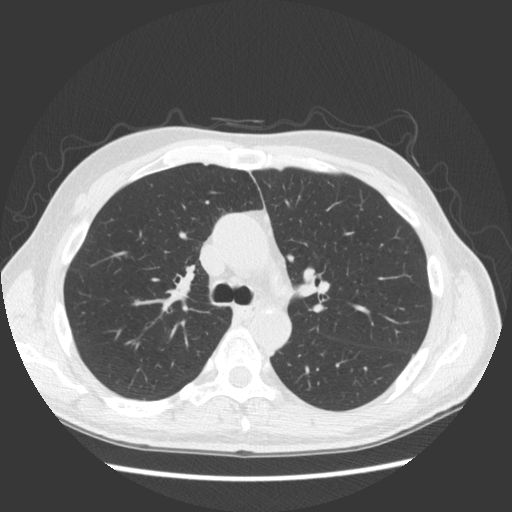
Chest CT (low-dose screening protocol), one axial image, second screening round (one year after baseline), lung window (W 1500 / L -600 HU), 2.5 mm slice thickness, slice 60 of 163 in the series. Male participant, aged 57 years at enrolment. Former smoker at enrolment.
Lesion marked by an expert reader, bounding box (x1, y1, x2, y2) in pixels: (154, 255, 204, 299). The screening reader recorded 3 non-calcified nodules or masses ≥4 mm on this exam; which of them this box marks is not recorded. Participant outcome: lung cancer diagnosed 264 days after this screen — adenocarcinoma, NOS, right upper lobe, poorly differentiated (G3), stage IB (AJCC 6th edition), 25 mm at pathology.